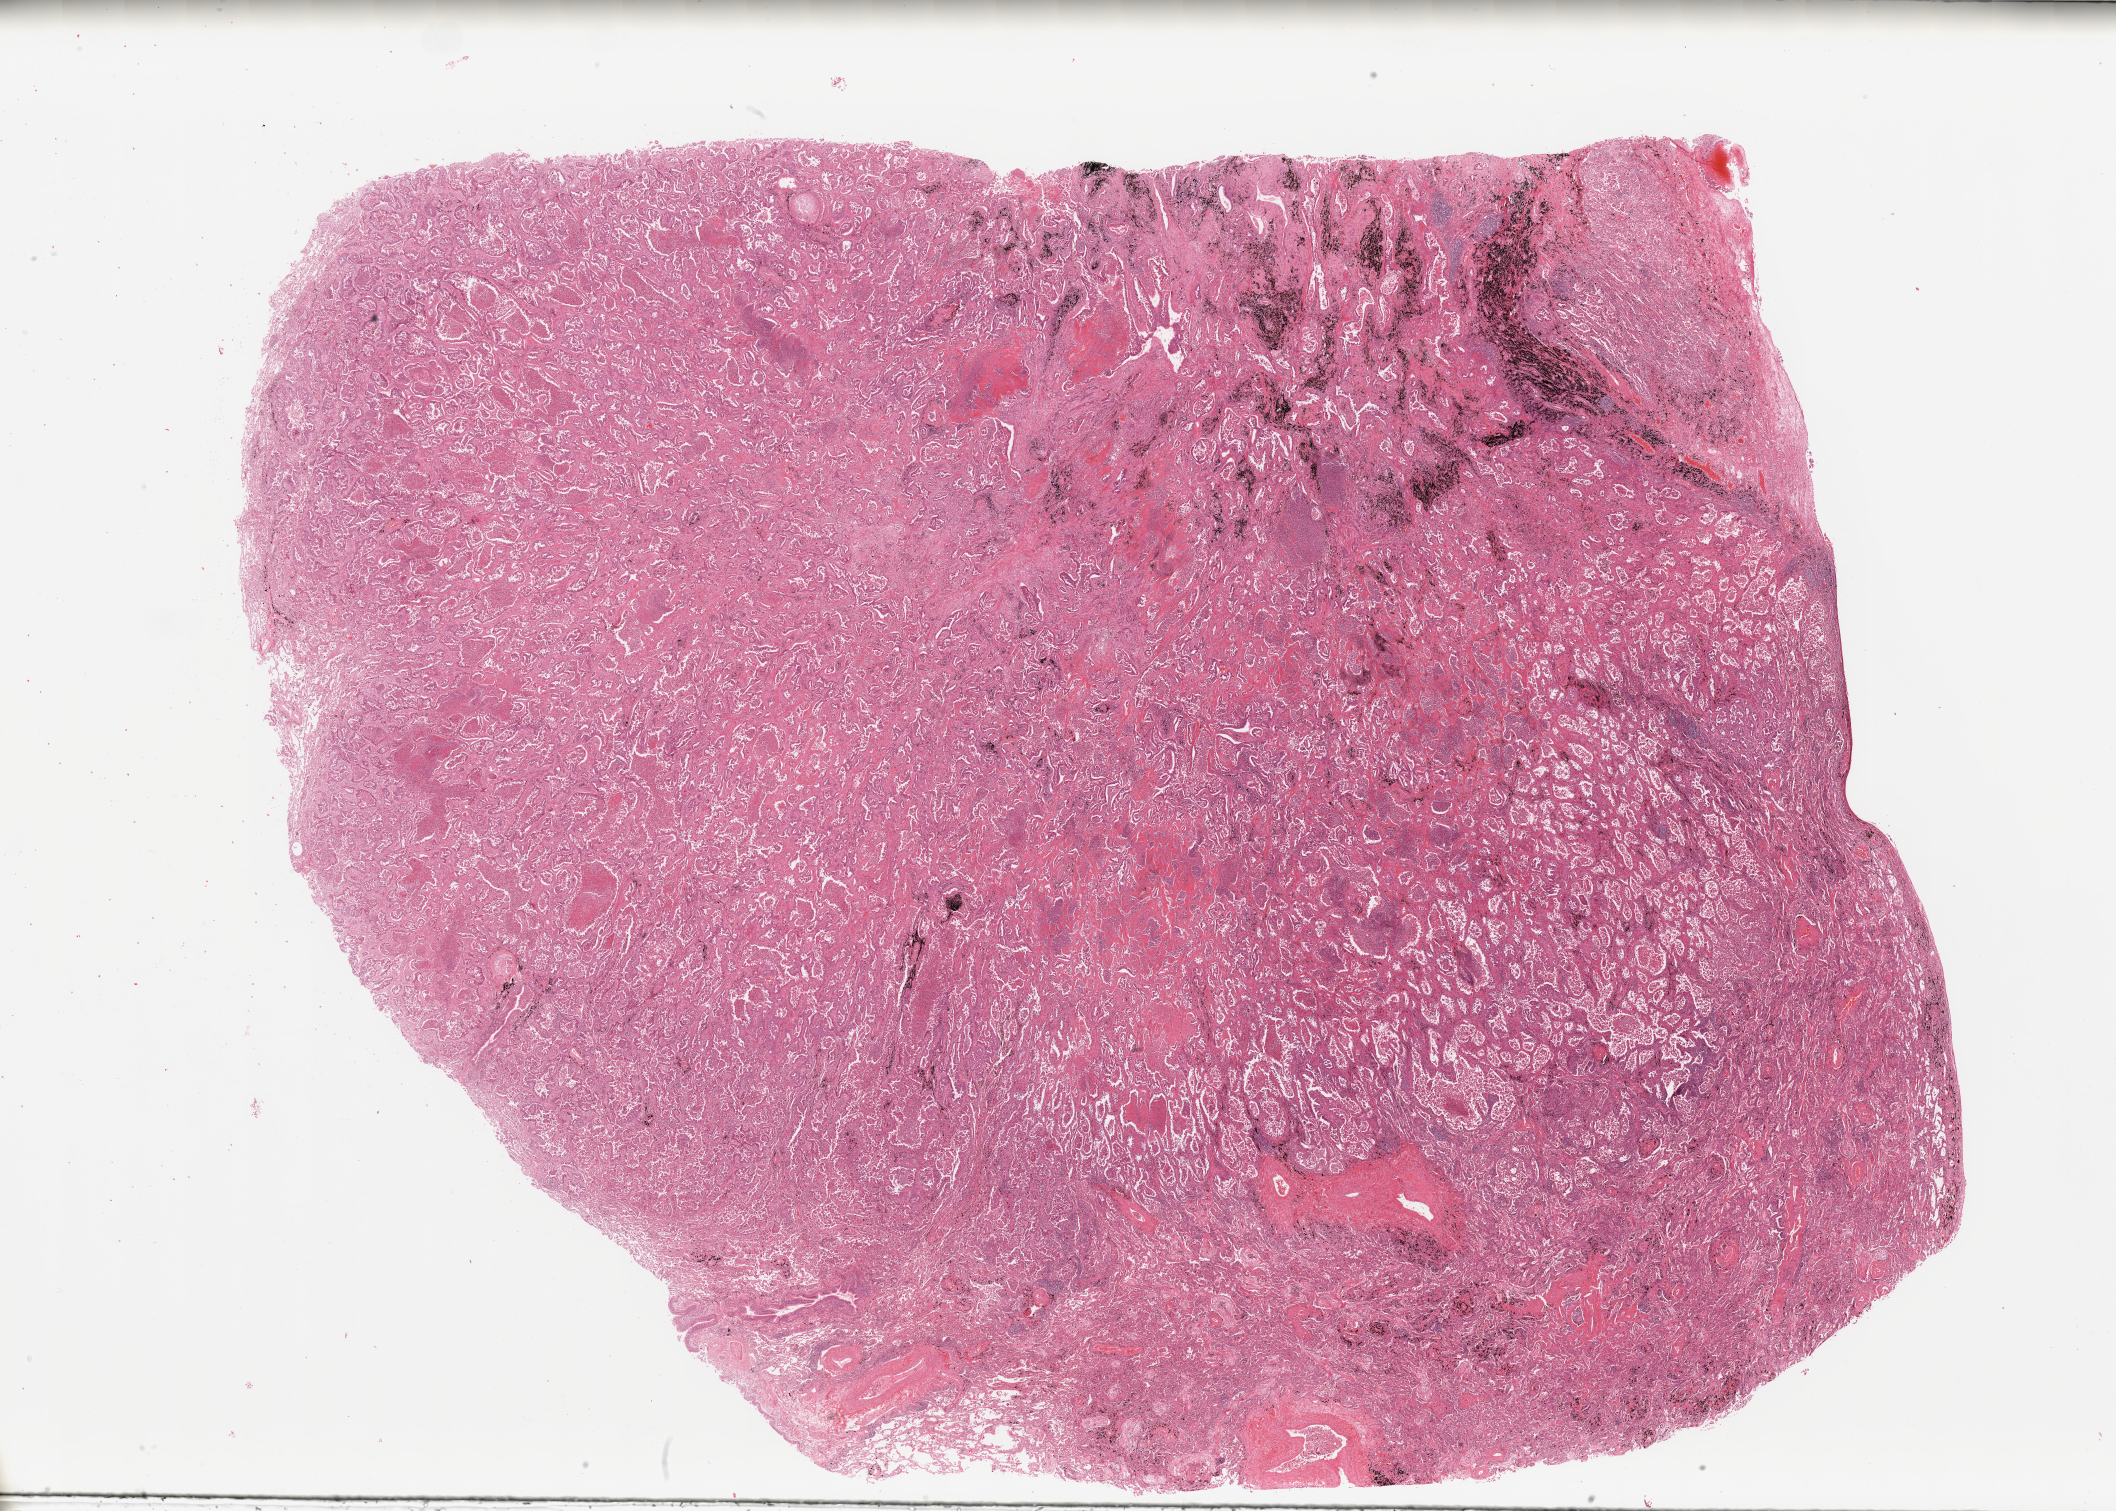
Whole-slide histology image, Hematoxylin and eosin (H&E) stained, whole scanned area (about 33.5 x 23.9 mm, from a 20x scan) shown as a low-resolution overview; tumour tissue sample, lung. Male, 69 y/o. Histologic grade: G2 (moderately differentiated).
AJCC pathologic stage: IB. Diagnosis: Adenocarcinoma, NOS. Primary tumour site (as recorded): left lower lobe.